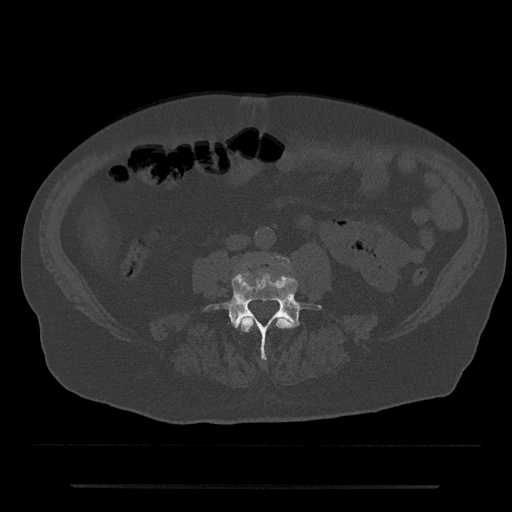
CT including the spine, one axial slice; slice 365 of 797 in the series (ordered by position); bone window (W 1800 / L 400 HU); 512 × 512 image matrix. Patient: male, 80 years. From the clinical record (not read from this slice): primary cancer: prostate; vertebrae with lytic lesions (as recorded): L1, T11.
Outlined on this slice (semi-automatically segmented with operator editing):
- L3 vertebra: bounding box (x1, y1, x2, y2) in pixels: (238, 317, 293, 333)
- L4 vertebra: (204, 271, 322, 360)